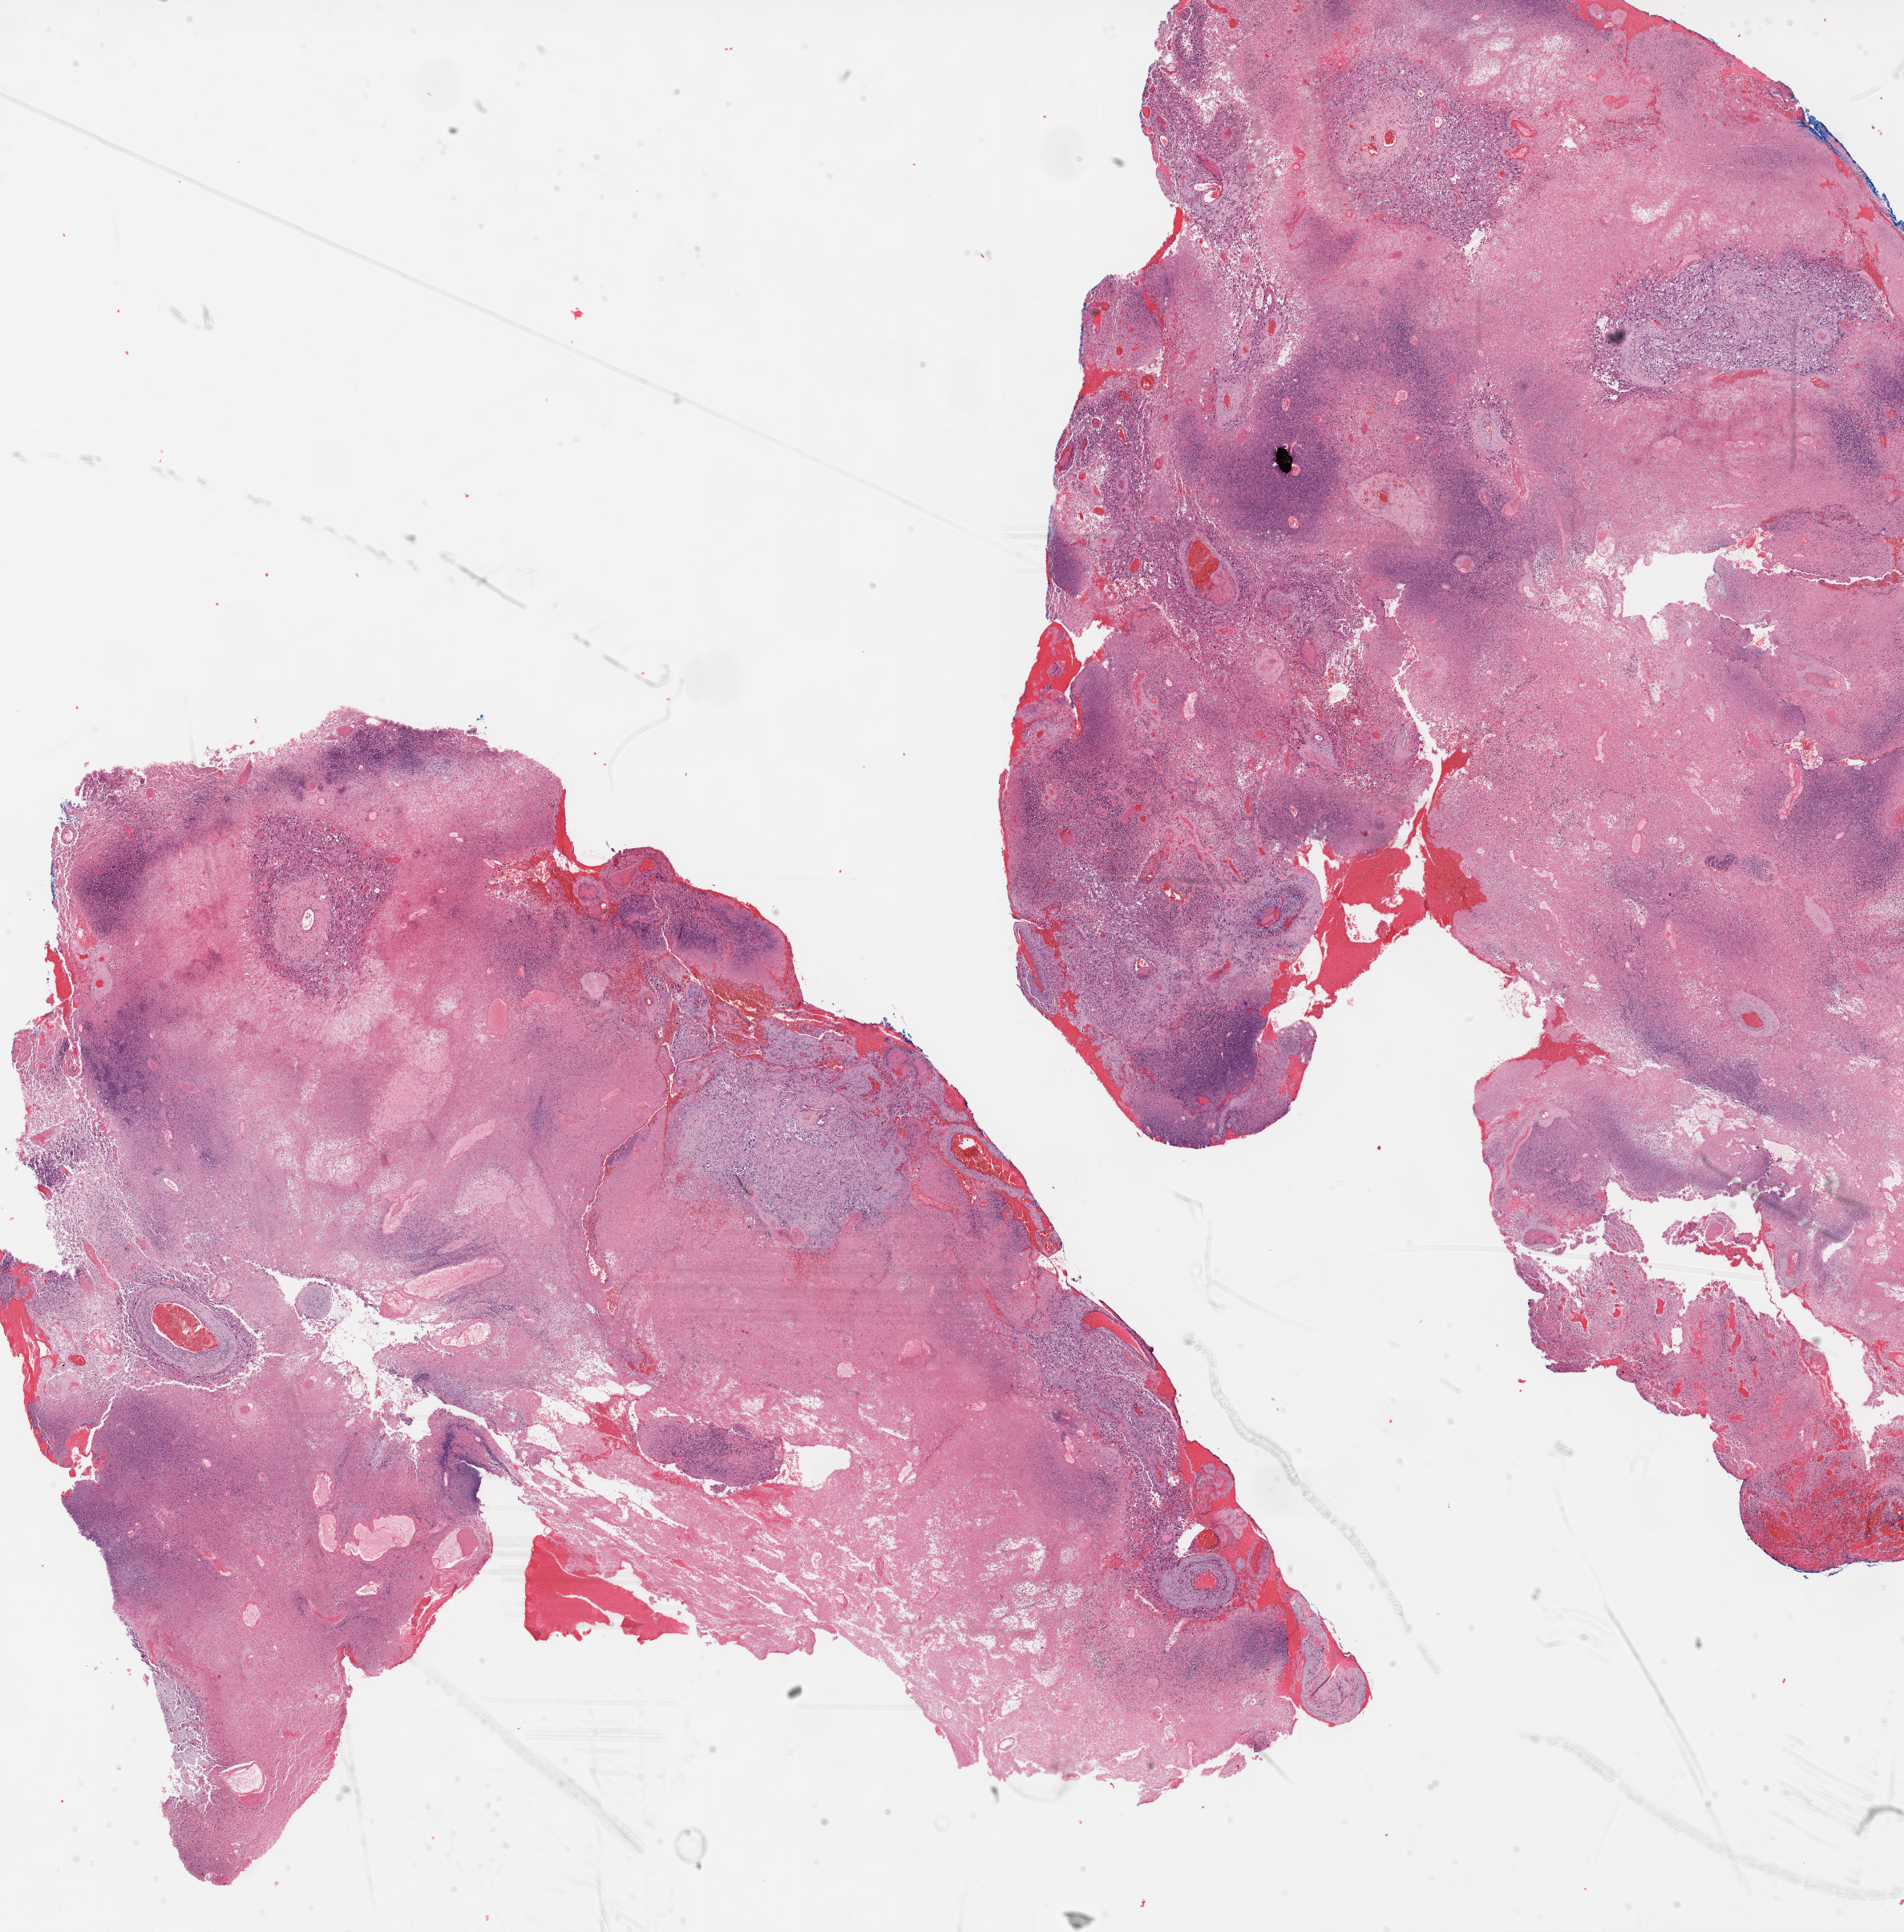
H&E-stained whole-slide image — a low-resolution overview of the entire scanned area, about 19.1 x 19.3 mm. Formalin-fixed paraffin-embedded (FFPE) diagnostic section. Sample: primary tumour, brain. Male, age 66 years at initial diagnosis.
Histologic diagnosis: Glioblastoma.